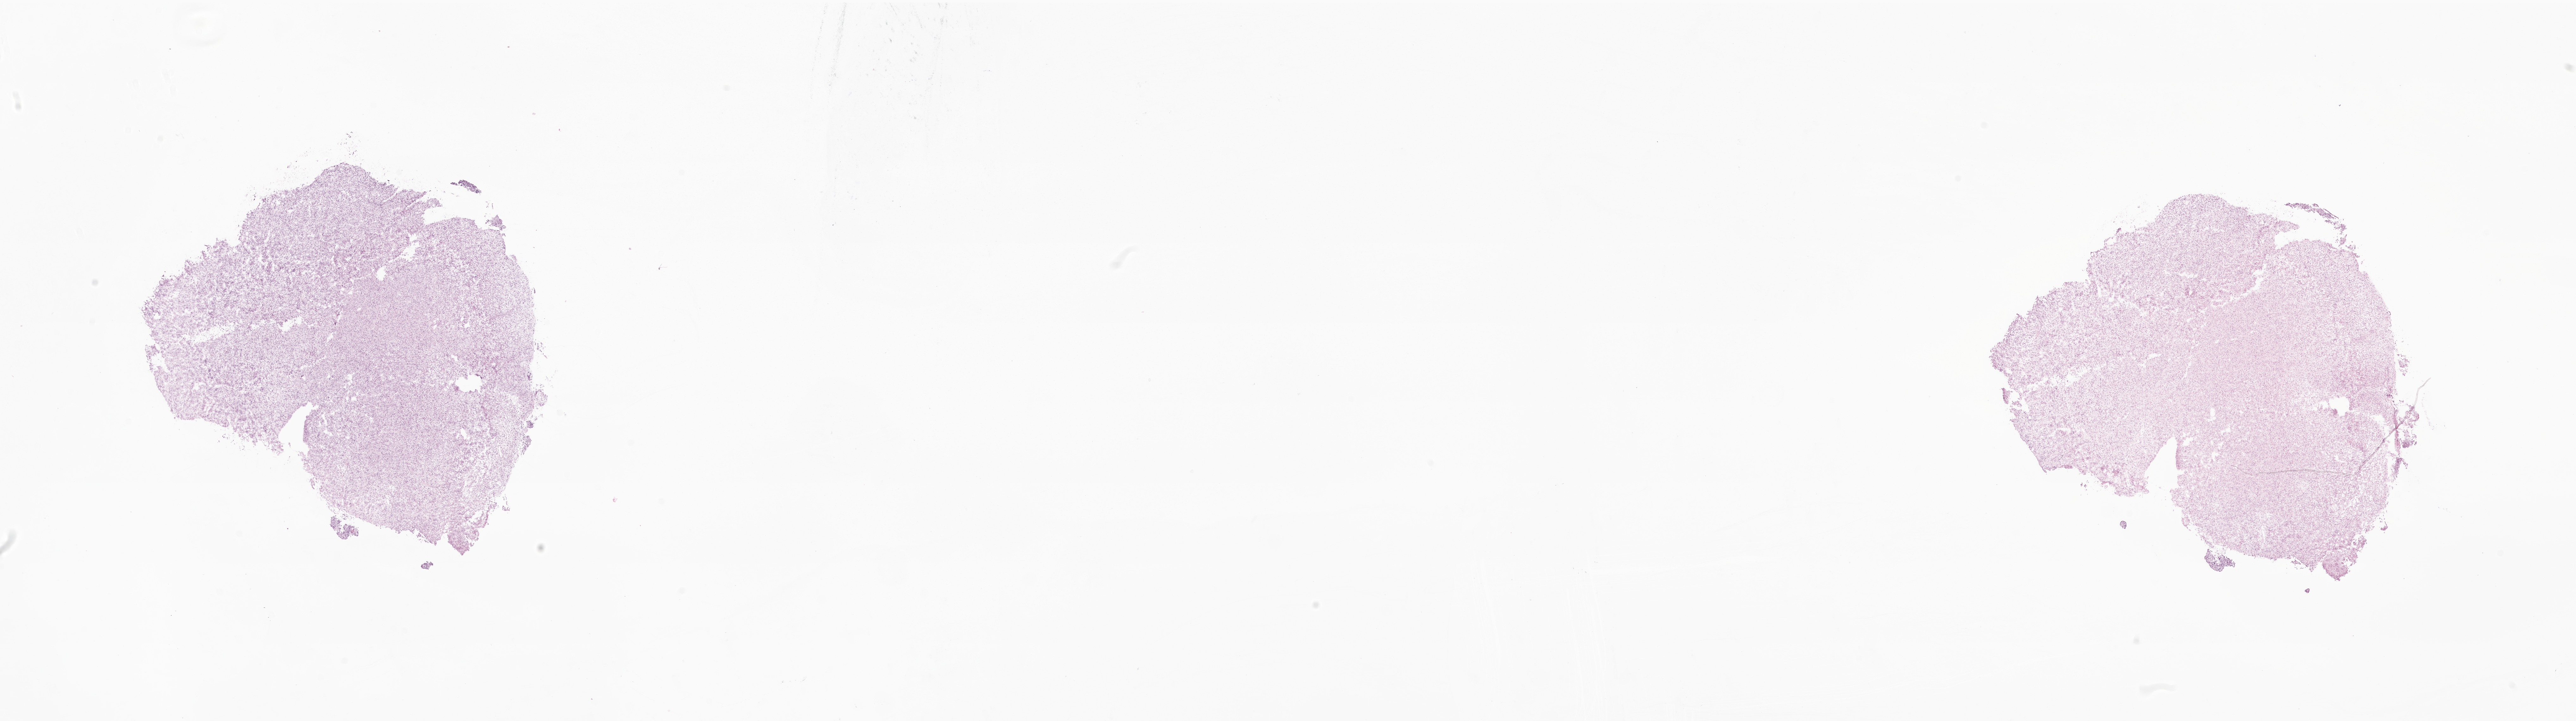
Haematoxylin and eosin whole-slide image of tumor tissue from the brain — whole scanned area (about 34.3 x 9.6 mm) shown as a low-resolution overview; cryosection (OCT / tissue freezing medium). Patient male; age 53 months (4 years 5 months).
Diagnosis: Neoplasm, malignant.